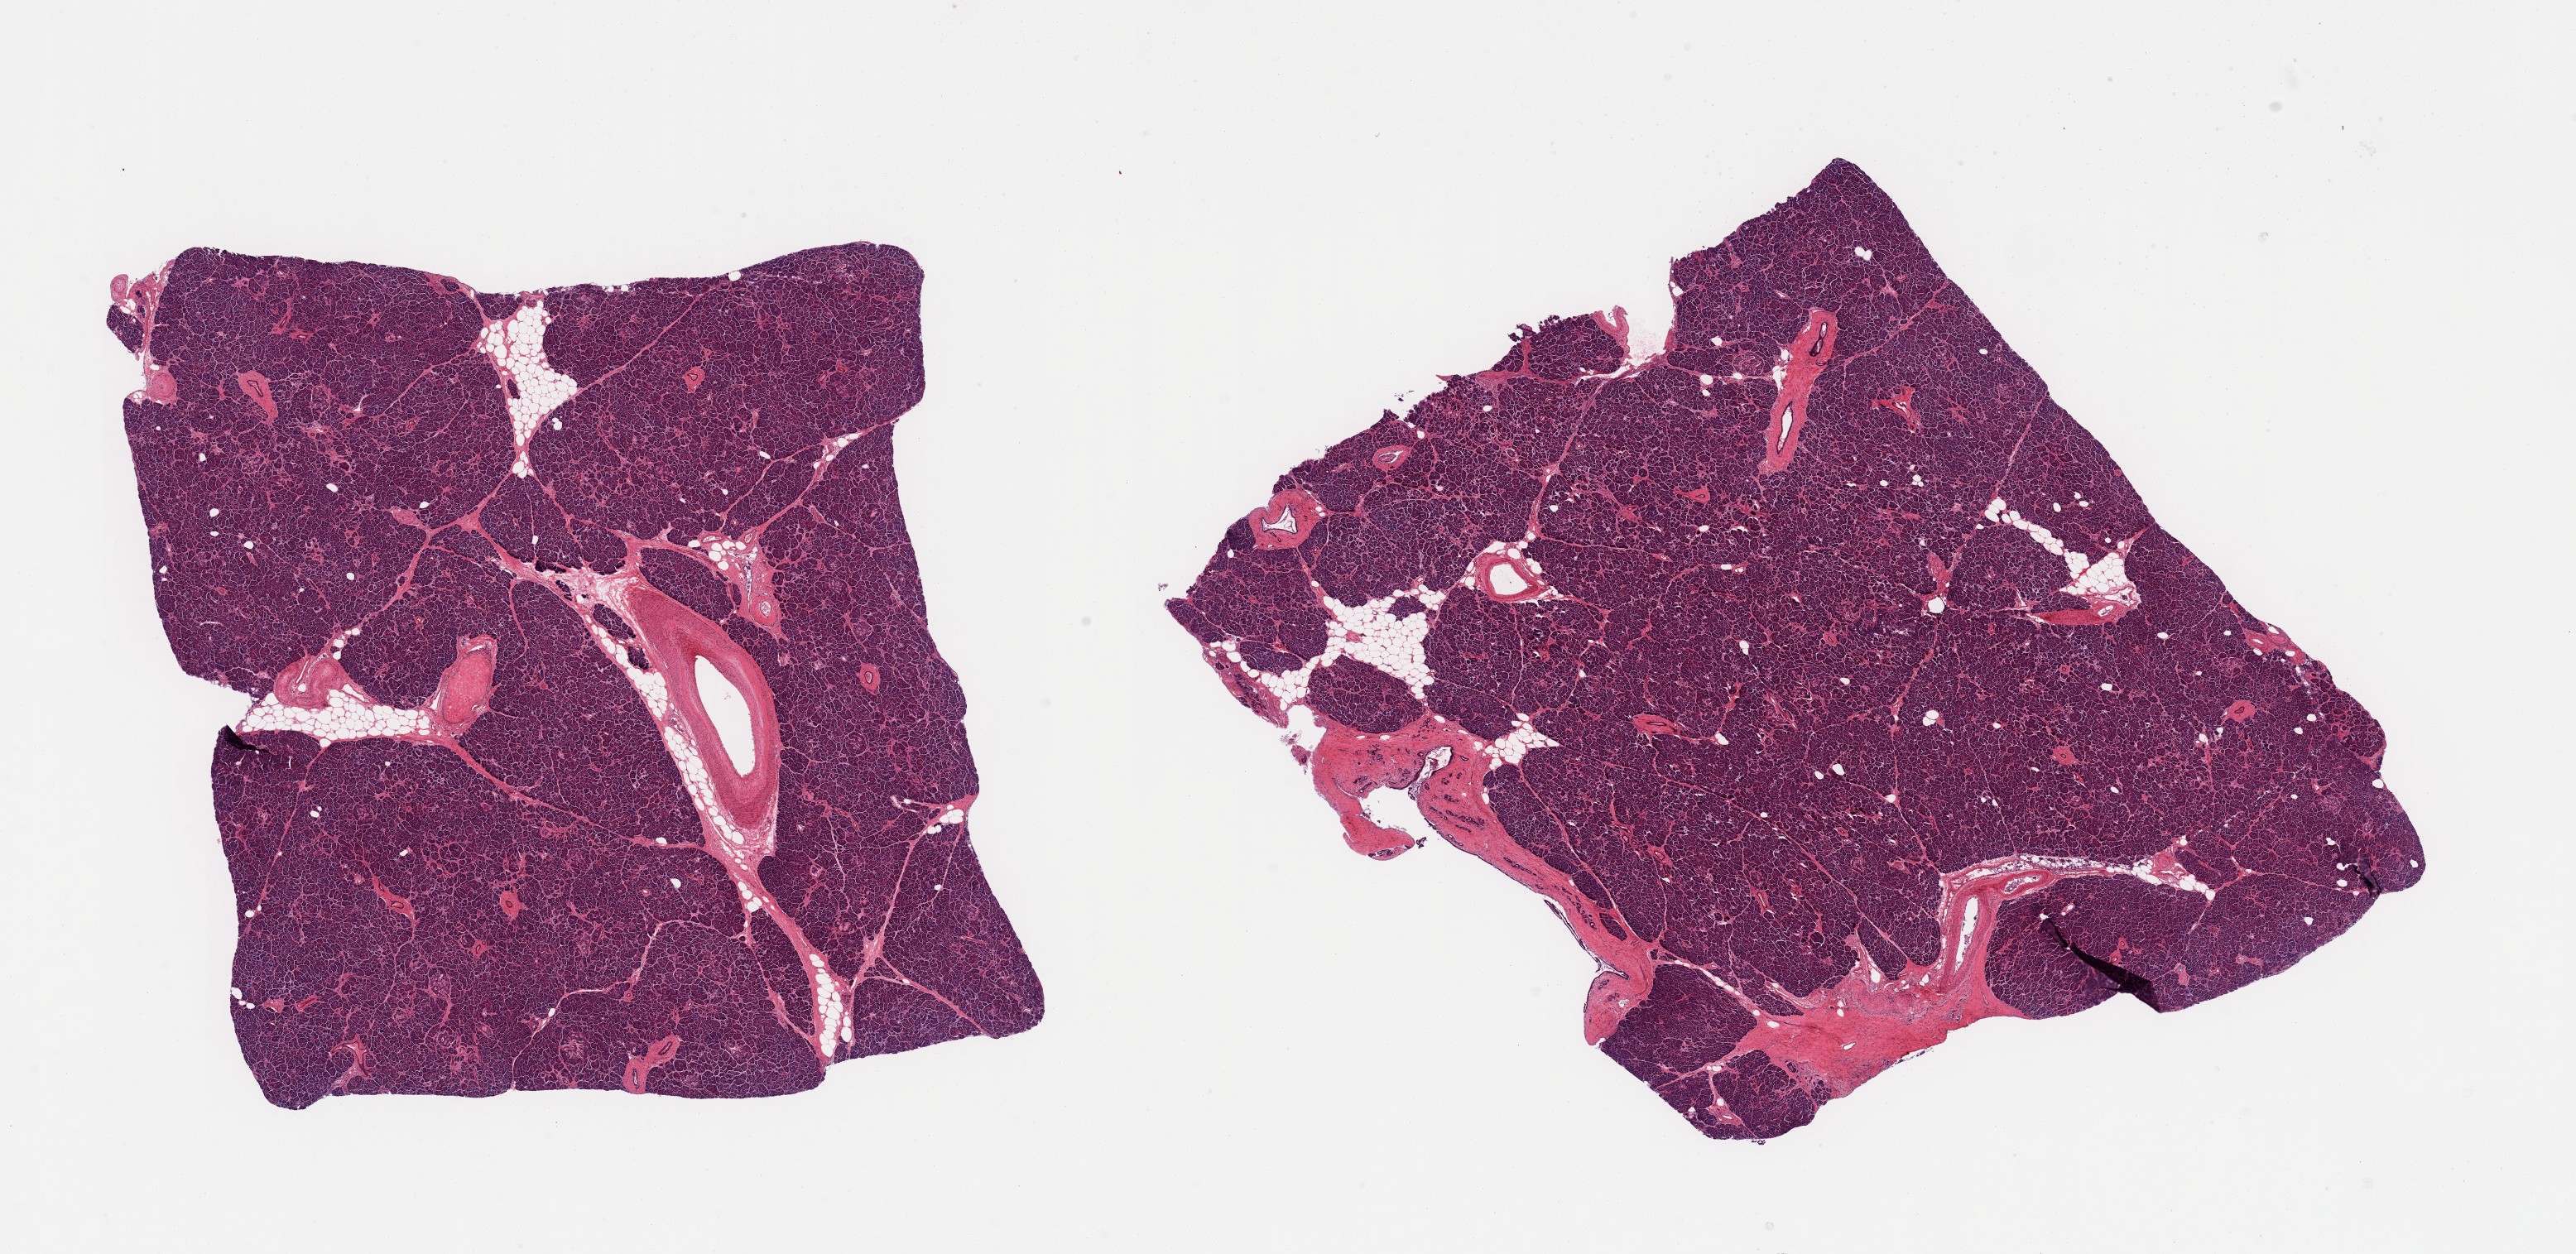
Whole-slide image, haematoxylin and eosin stain — low-resolution overview of the scanned area, about 24.6 x 12.0 mm; PAXgene-fixed, paraffin-embedded tissue; sampled site (target tissue): pancreas; donor tissue sample. Donor: male.
Pathologist's review note for this sample: 2 pieces; 10% internal fat; 10% large blood vessels & ducts; block 26 trimmed.